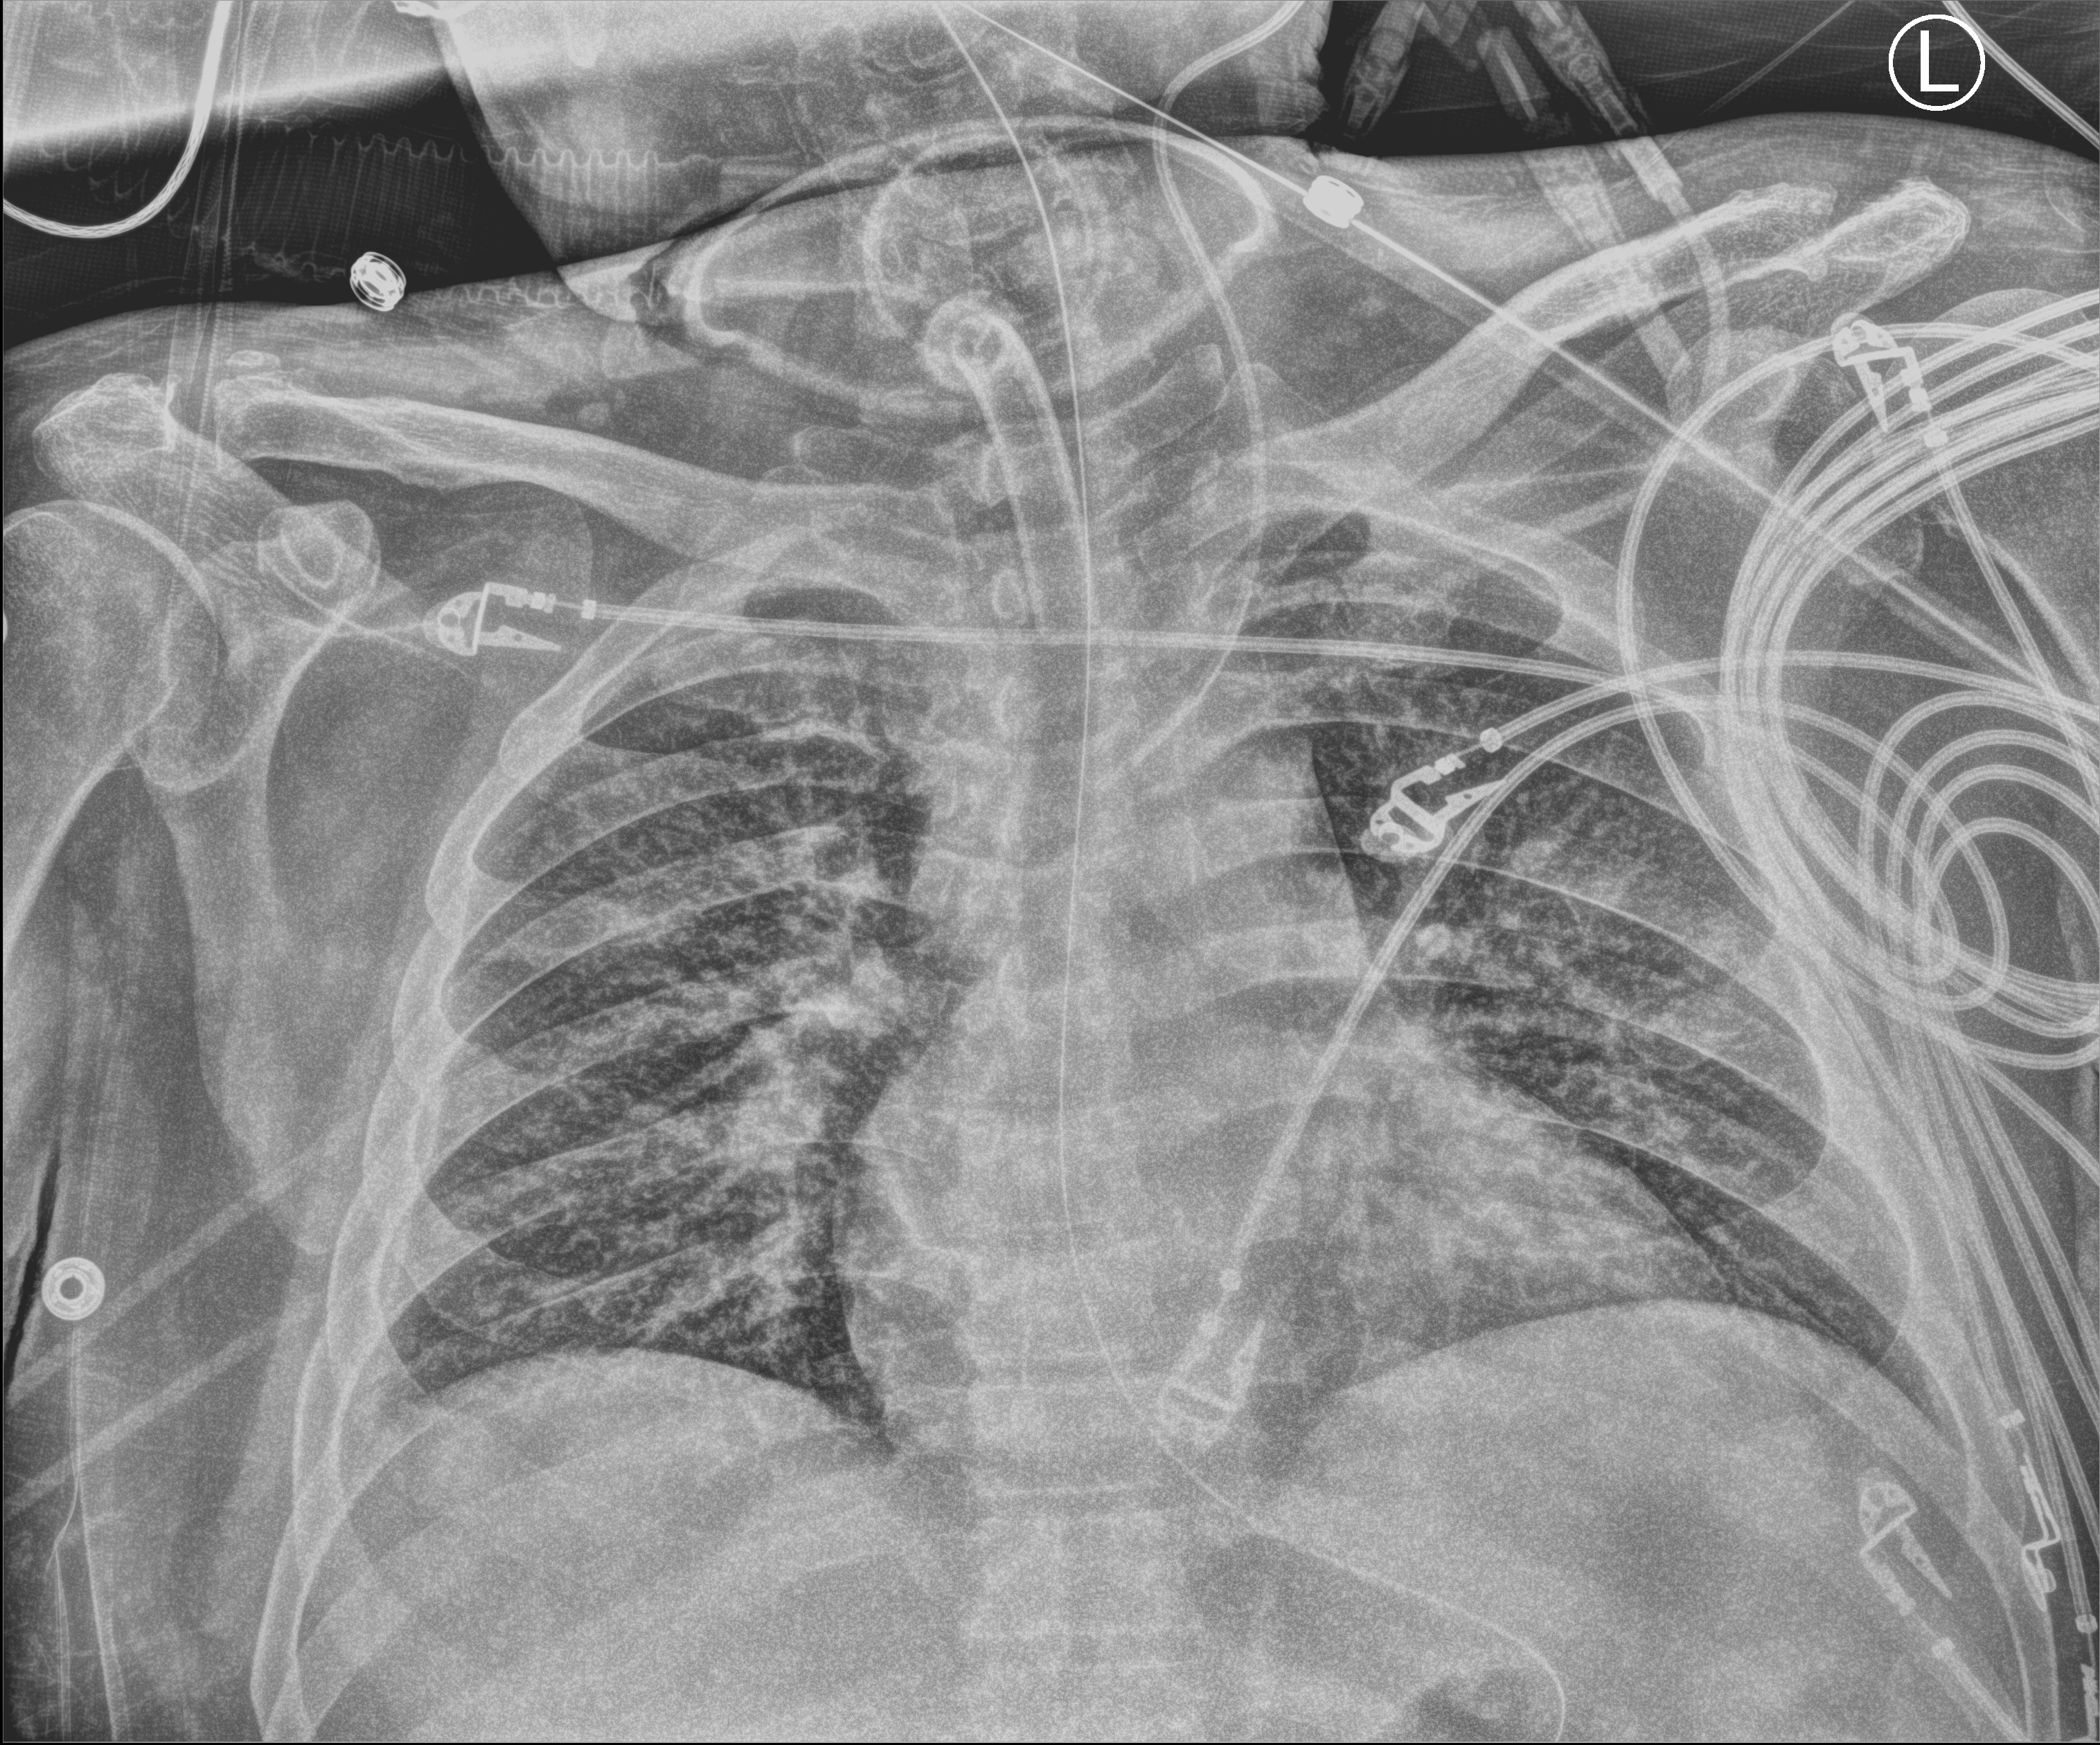
Bedside chest radiograph (computed radiography); anteroposterior (AP) projection. Patient hospitalised with COVID-19; male, aged 18–59 years.
Hospital-stay facts (about this admission, not read from this image; timing relative to this image not recorded):
- mechanically ventilated during this hospital stay: yes